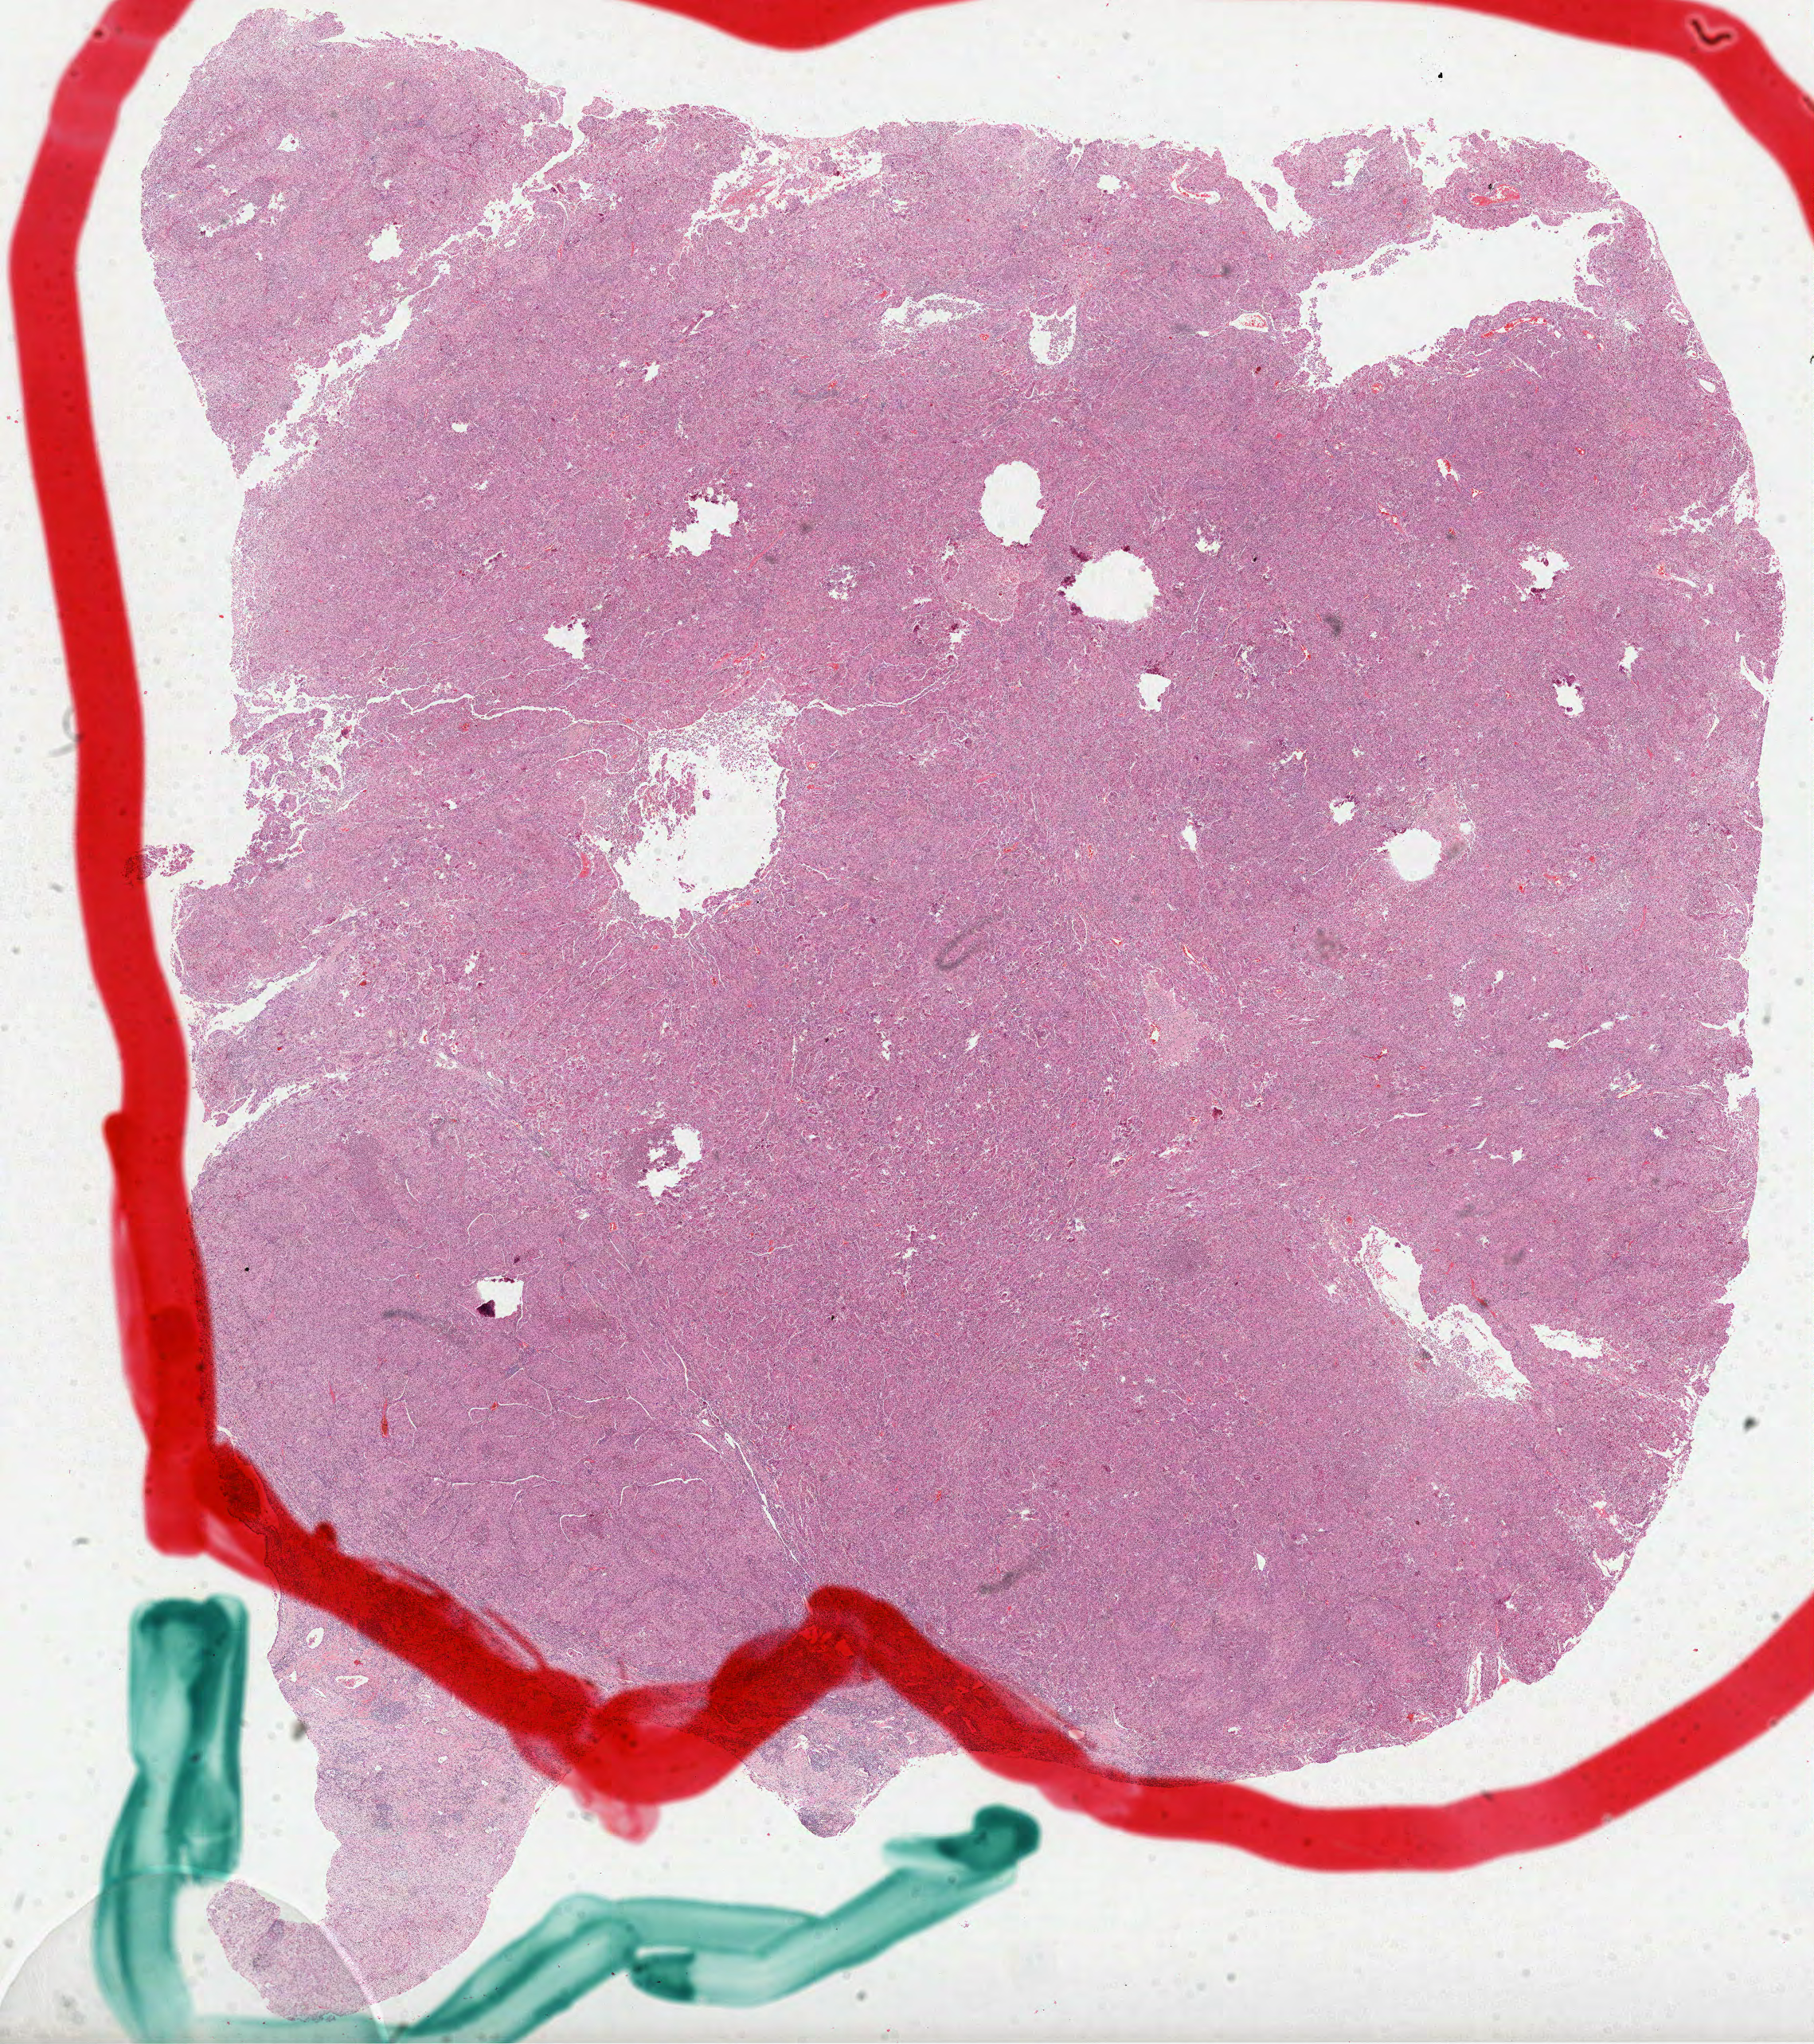
H&E-stained whole-slide image — a low-resolution overview of the entire scanned area, about 18.4 x 20.7 mm (from a 40x scan); FFPE section; sample: primary tumour, lung. Male, age 70 years at initial diagnosis.
Histologic diagnosis: Adenocarcinoma, NOS (lower lobe, lung). AJCC pathologic stage: IIA (7th edition).